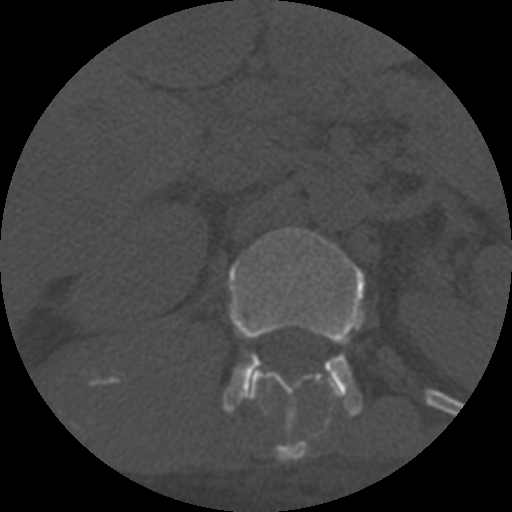
CT including the spine, one axial slice; position 298 of 708 along the scan axis; reconstruction kernel STANDARD; 120 kVp; one of 3 acquisitions stored at this slice position; bone window (W 1800 / L 400 HU); 1.25 mm slice thickness; 512 × 512 image matrix, field of view 160 × 160 mm. Patient age 55 years. Case-level facts recorded for this patient, not image findings: primary cancer: colon; vertebrae with lytic lesions (as recorded): T12, L1, L5.
Annotated regions visible in this slice (semi-automatic segmentation, software-assisted and operator-edited):
- L1 vertebra: box from (x=223, y=227) to (x=366, y=416) px
- T12 vertebra: (x=249, y=370)–(x=328, y=462)